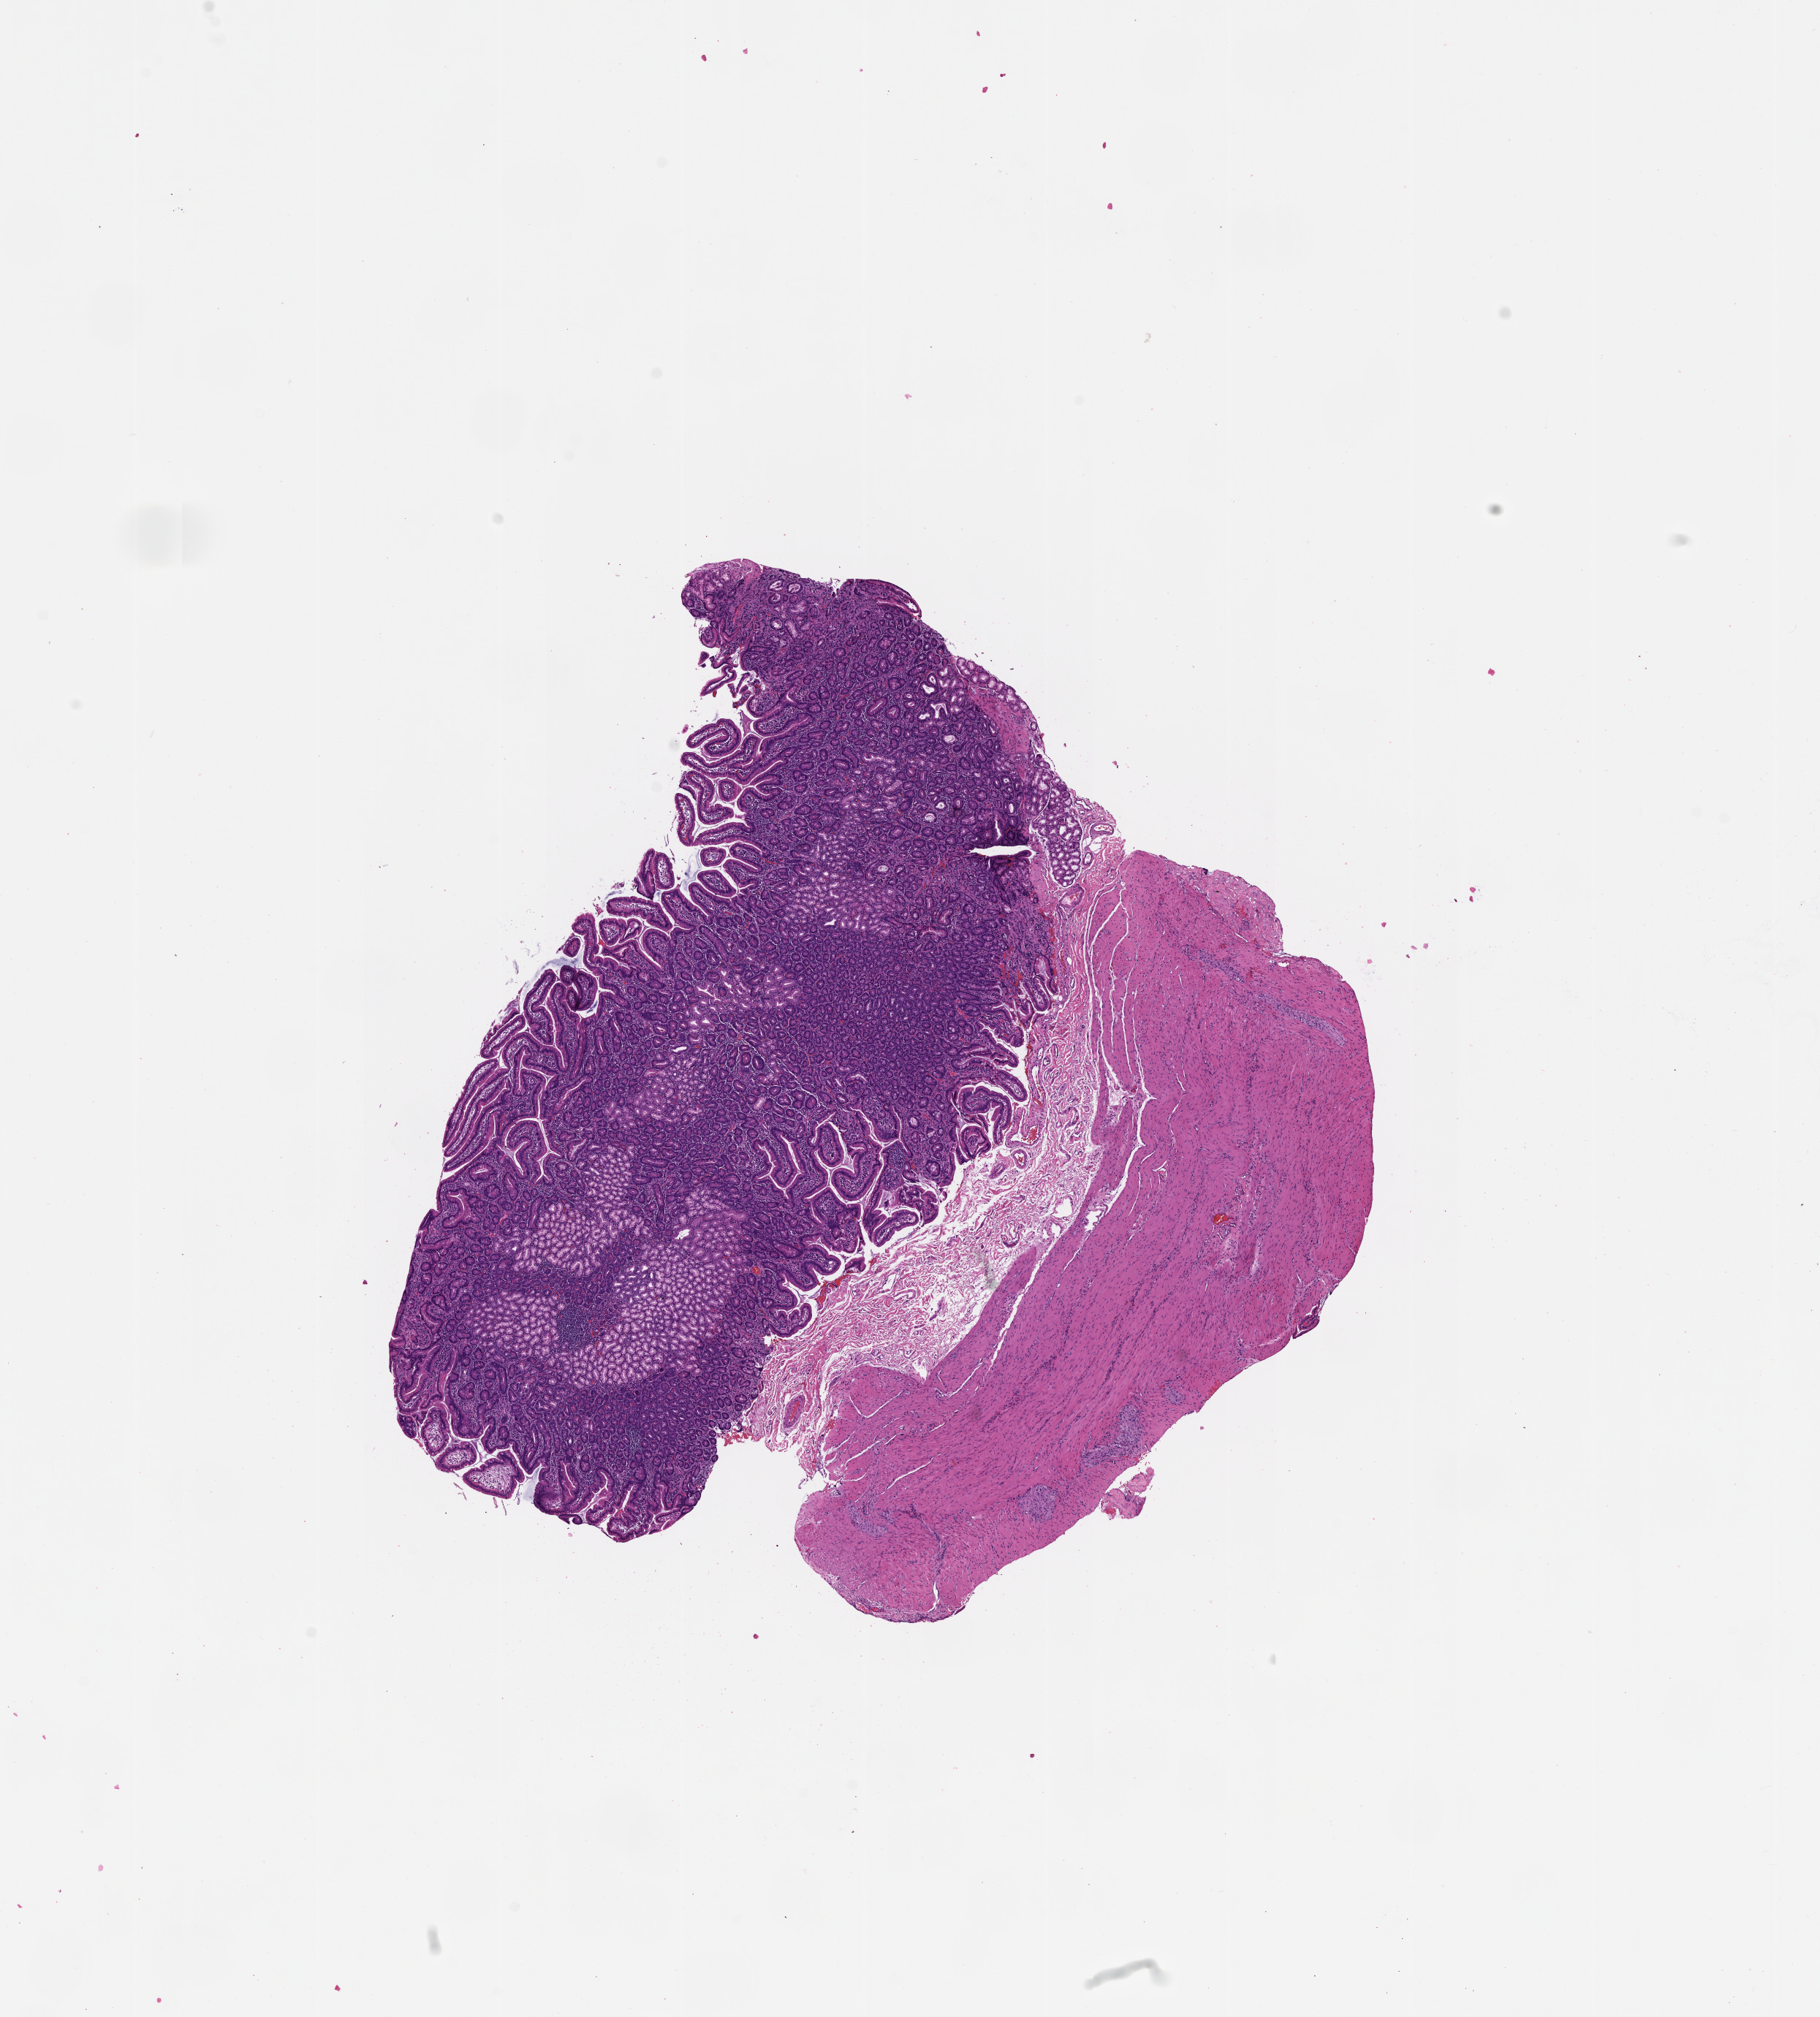
H&E whole-slide image — shown as a low-resolution overview of the whole scanned area (about 10.0 x 11.1 mm); normal (non-tumour) tissue sample, sampled site: pancreas. Patient: female, age 71 years.
- this section: normal (non-tumour) tissue from the same patient
- patient diagnosis: Infiltrating duct carcinoma, NOS